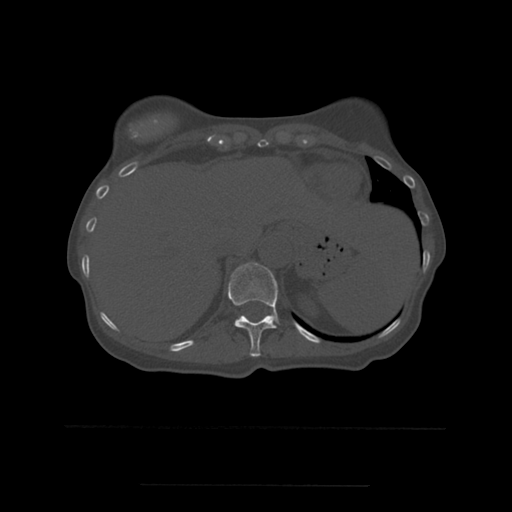
CT including the spine, one axial slice; bone window (W 1800 / L 400 HU); 1.25 mm slice thickness; 512 × 512 image matrix. Patient age 58 years. From the clinical record (not read from this slice): primary cancer: lung.
Structures marked on this image (semi-automatically segmented with operator editing):
- T11 vertebra: bounding box [x1, y1, x2, y2] px = [228, 263, 279, 357]